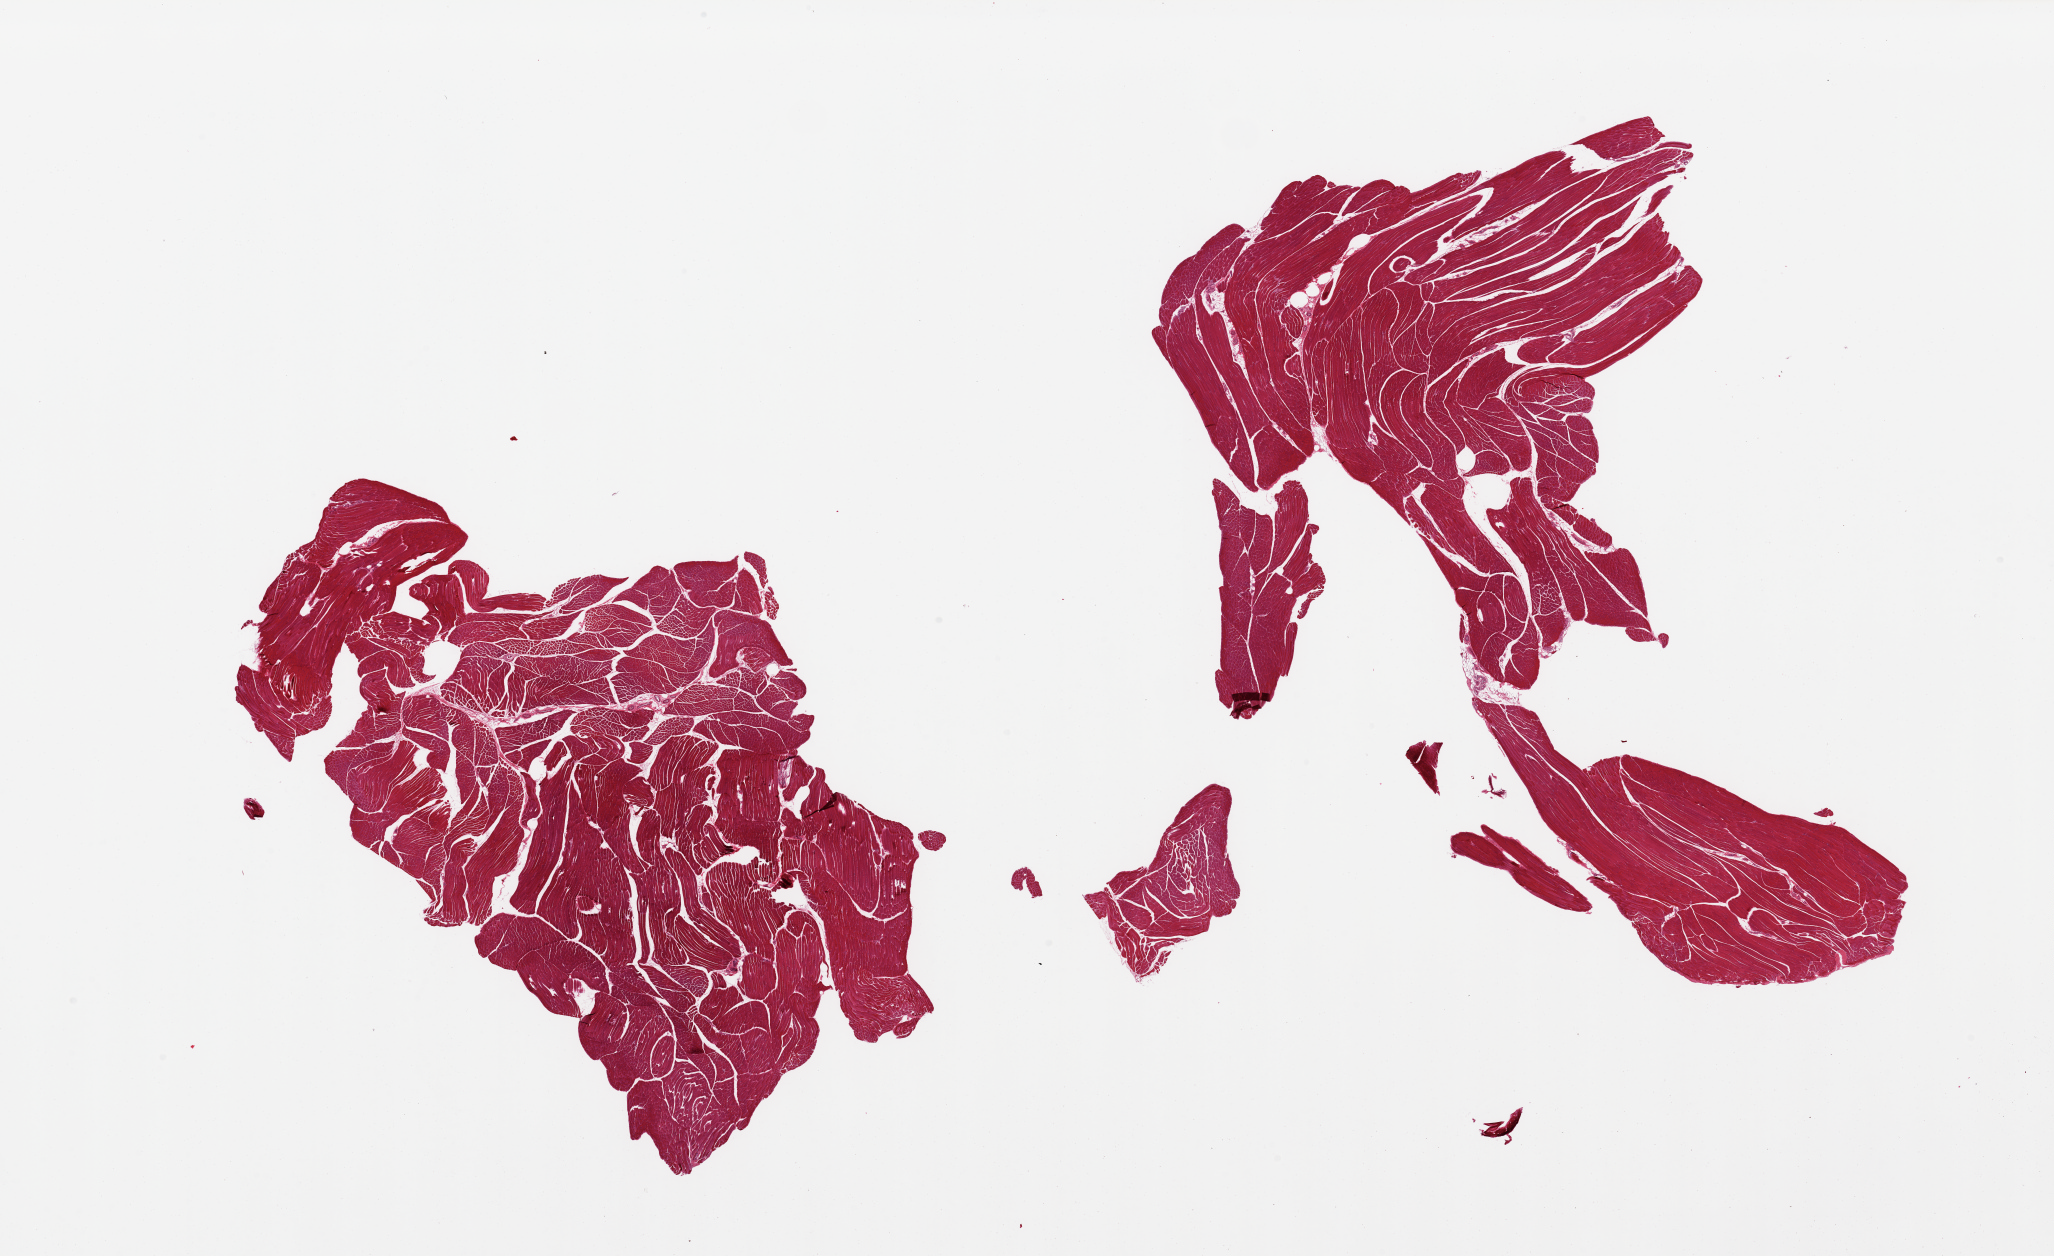
Whole-slide image, H&E stain — shown as a low-resolution overview of the whole scanned area (about 32.5 x 19.9 mm), PAXgene-fixed paraffin-embedded (PFPE) section, target tissue: skeletal muscle, tissue donor sample. Donor: female.
Reviewer comment on this tissue sample: 2 pieces, trace interstitial fat.